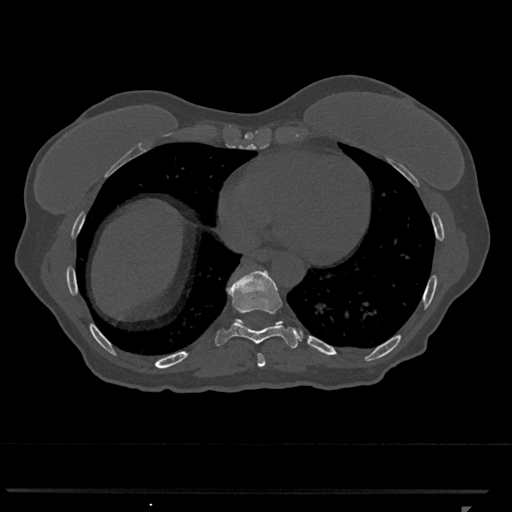
CT including the spine, one axial slice; position 614 of 793 along the scan axis; 120 kVp; bone window (W 1800 / L 400 HU); 0.5 mm slice thickness; 512 × 512 image matrix, field of view 380 × 380 mm. Patient: female, 62 years. Case-level facts recorded for this patient, not image findings: primary cancer: renal.
Outlined on this slice (semi-automatic segmentation, software-assisted and operator-edited):
- T10 vertebra: bounding box (x1, y1, x2, y2) in pixels: (240, 319, 283, 325)
- T8 vertebra: (257, 353, 266, 367)
- T9 vertebra: (215, 271, 300, 349)